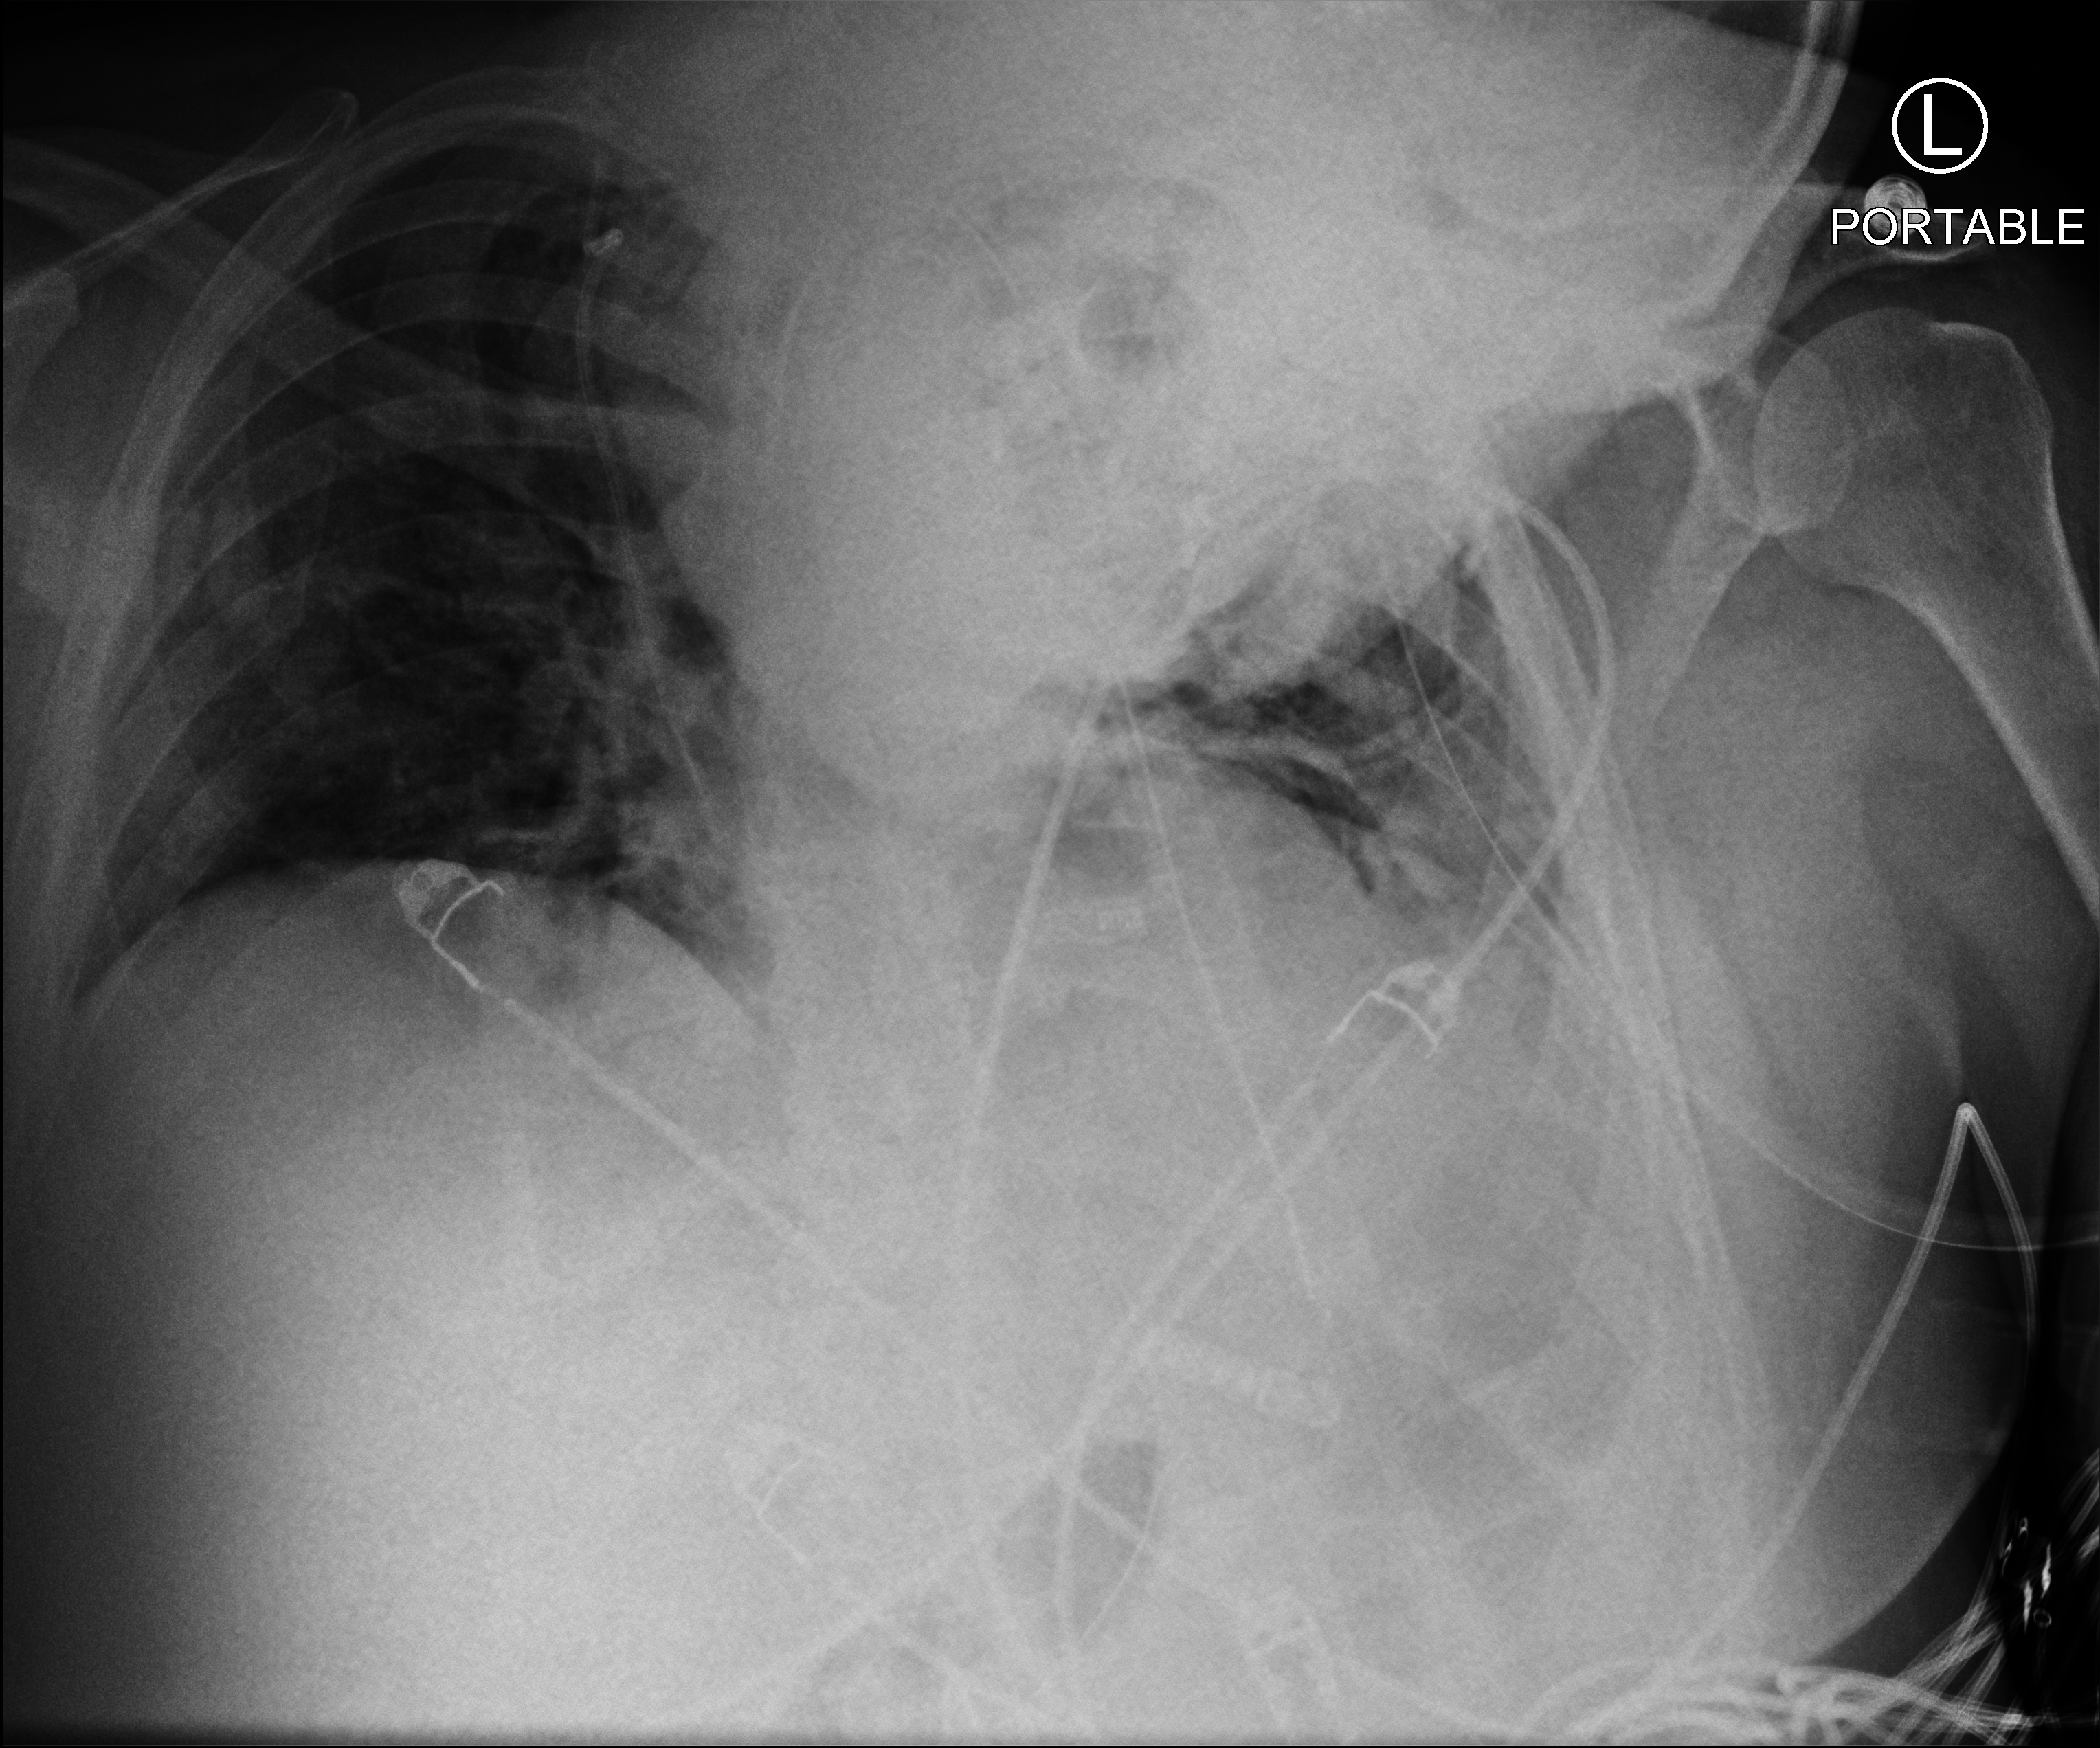
Chest X-ray (portable); anteroposterior (AP) projection. Male patient hospitalised with COVID-19, age 18–59 years.
Hospital-stay facts (about this admission, not read from this image; timing relative to this image not recorded): admitted to intensive care during this hospital stay: yes; mechanically ventilated during this hospital stay: yes.